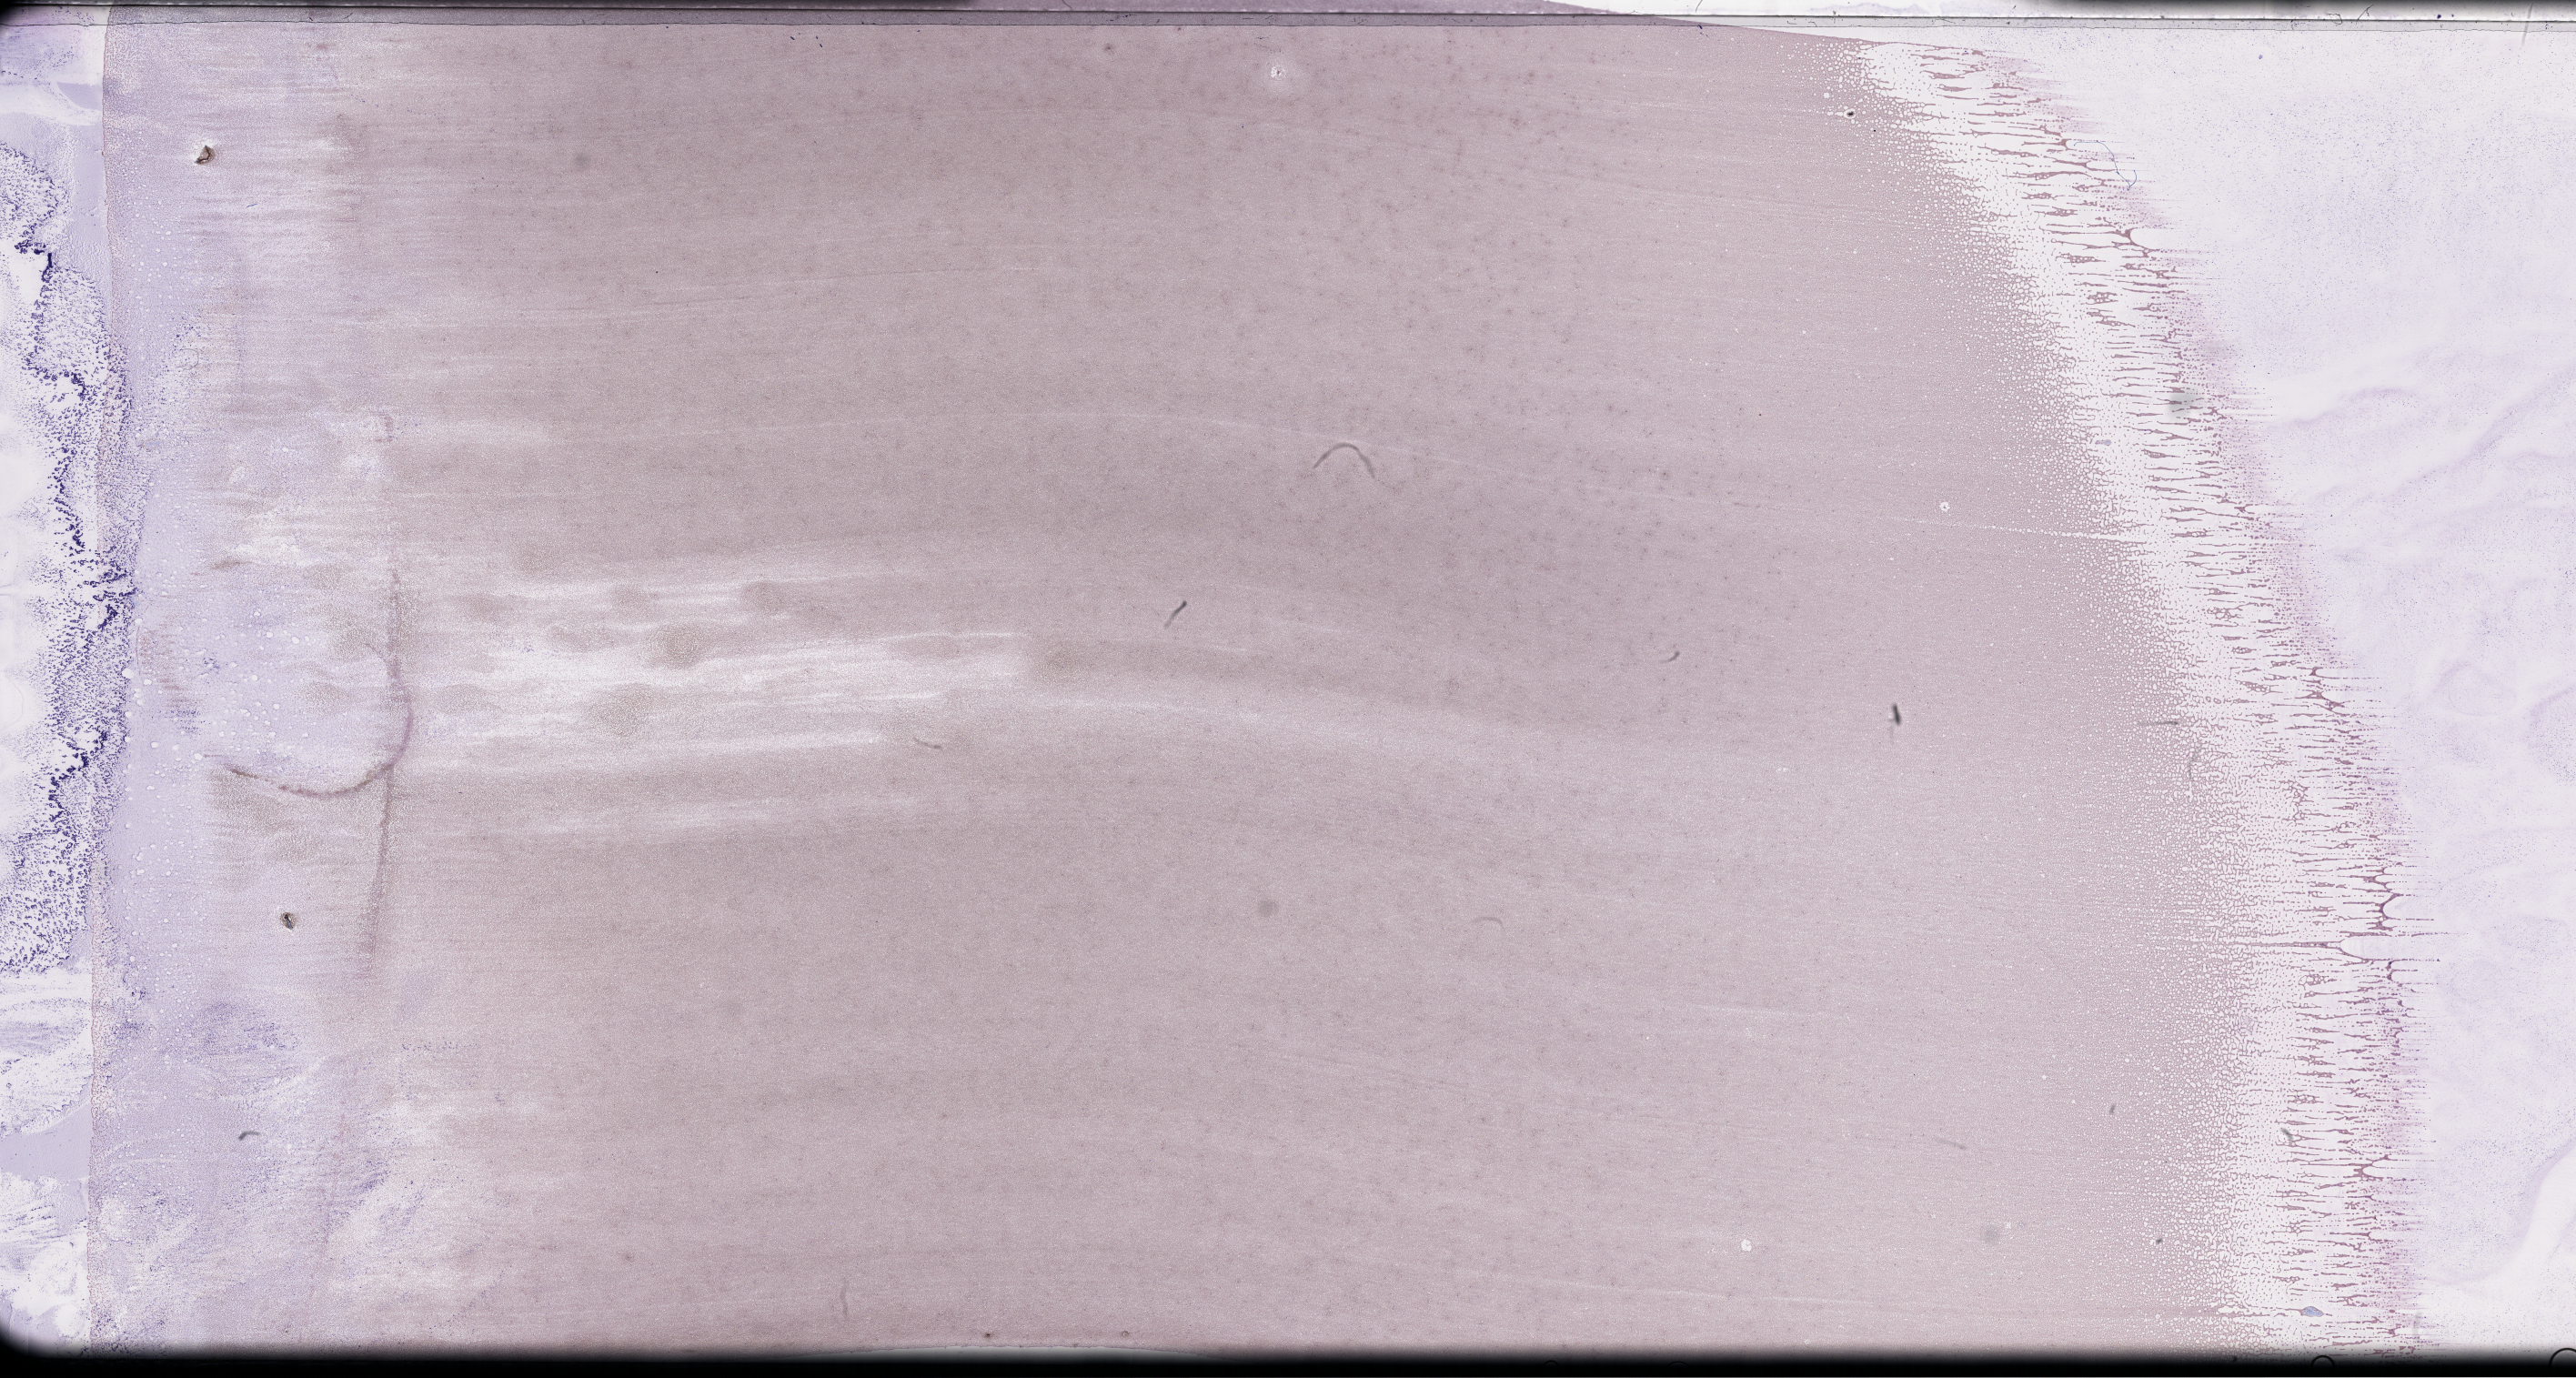
Whole-slide image of a whole blood smear, Wright–Giemsa stain — a low-resolution overview of the entire scanned area, about 45.7 x 24.5 mm. Patient sex: female.
- from a patient with: Plasma Cell Myeloma